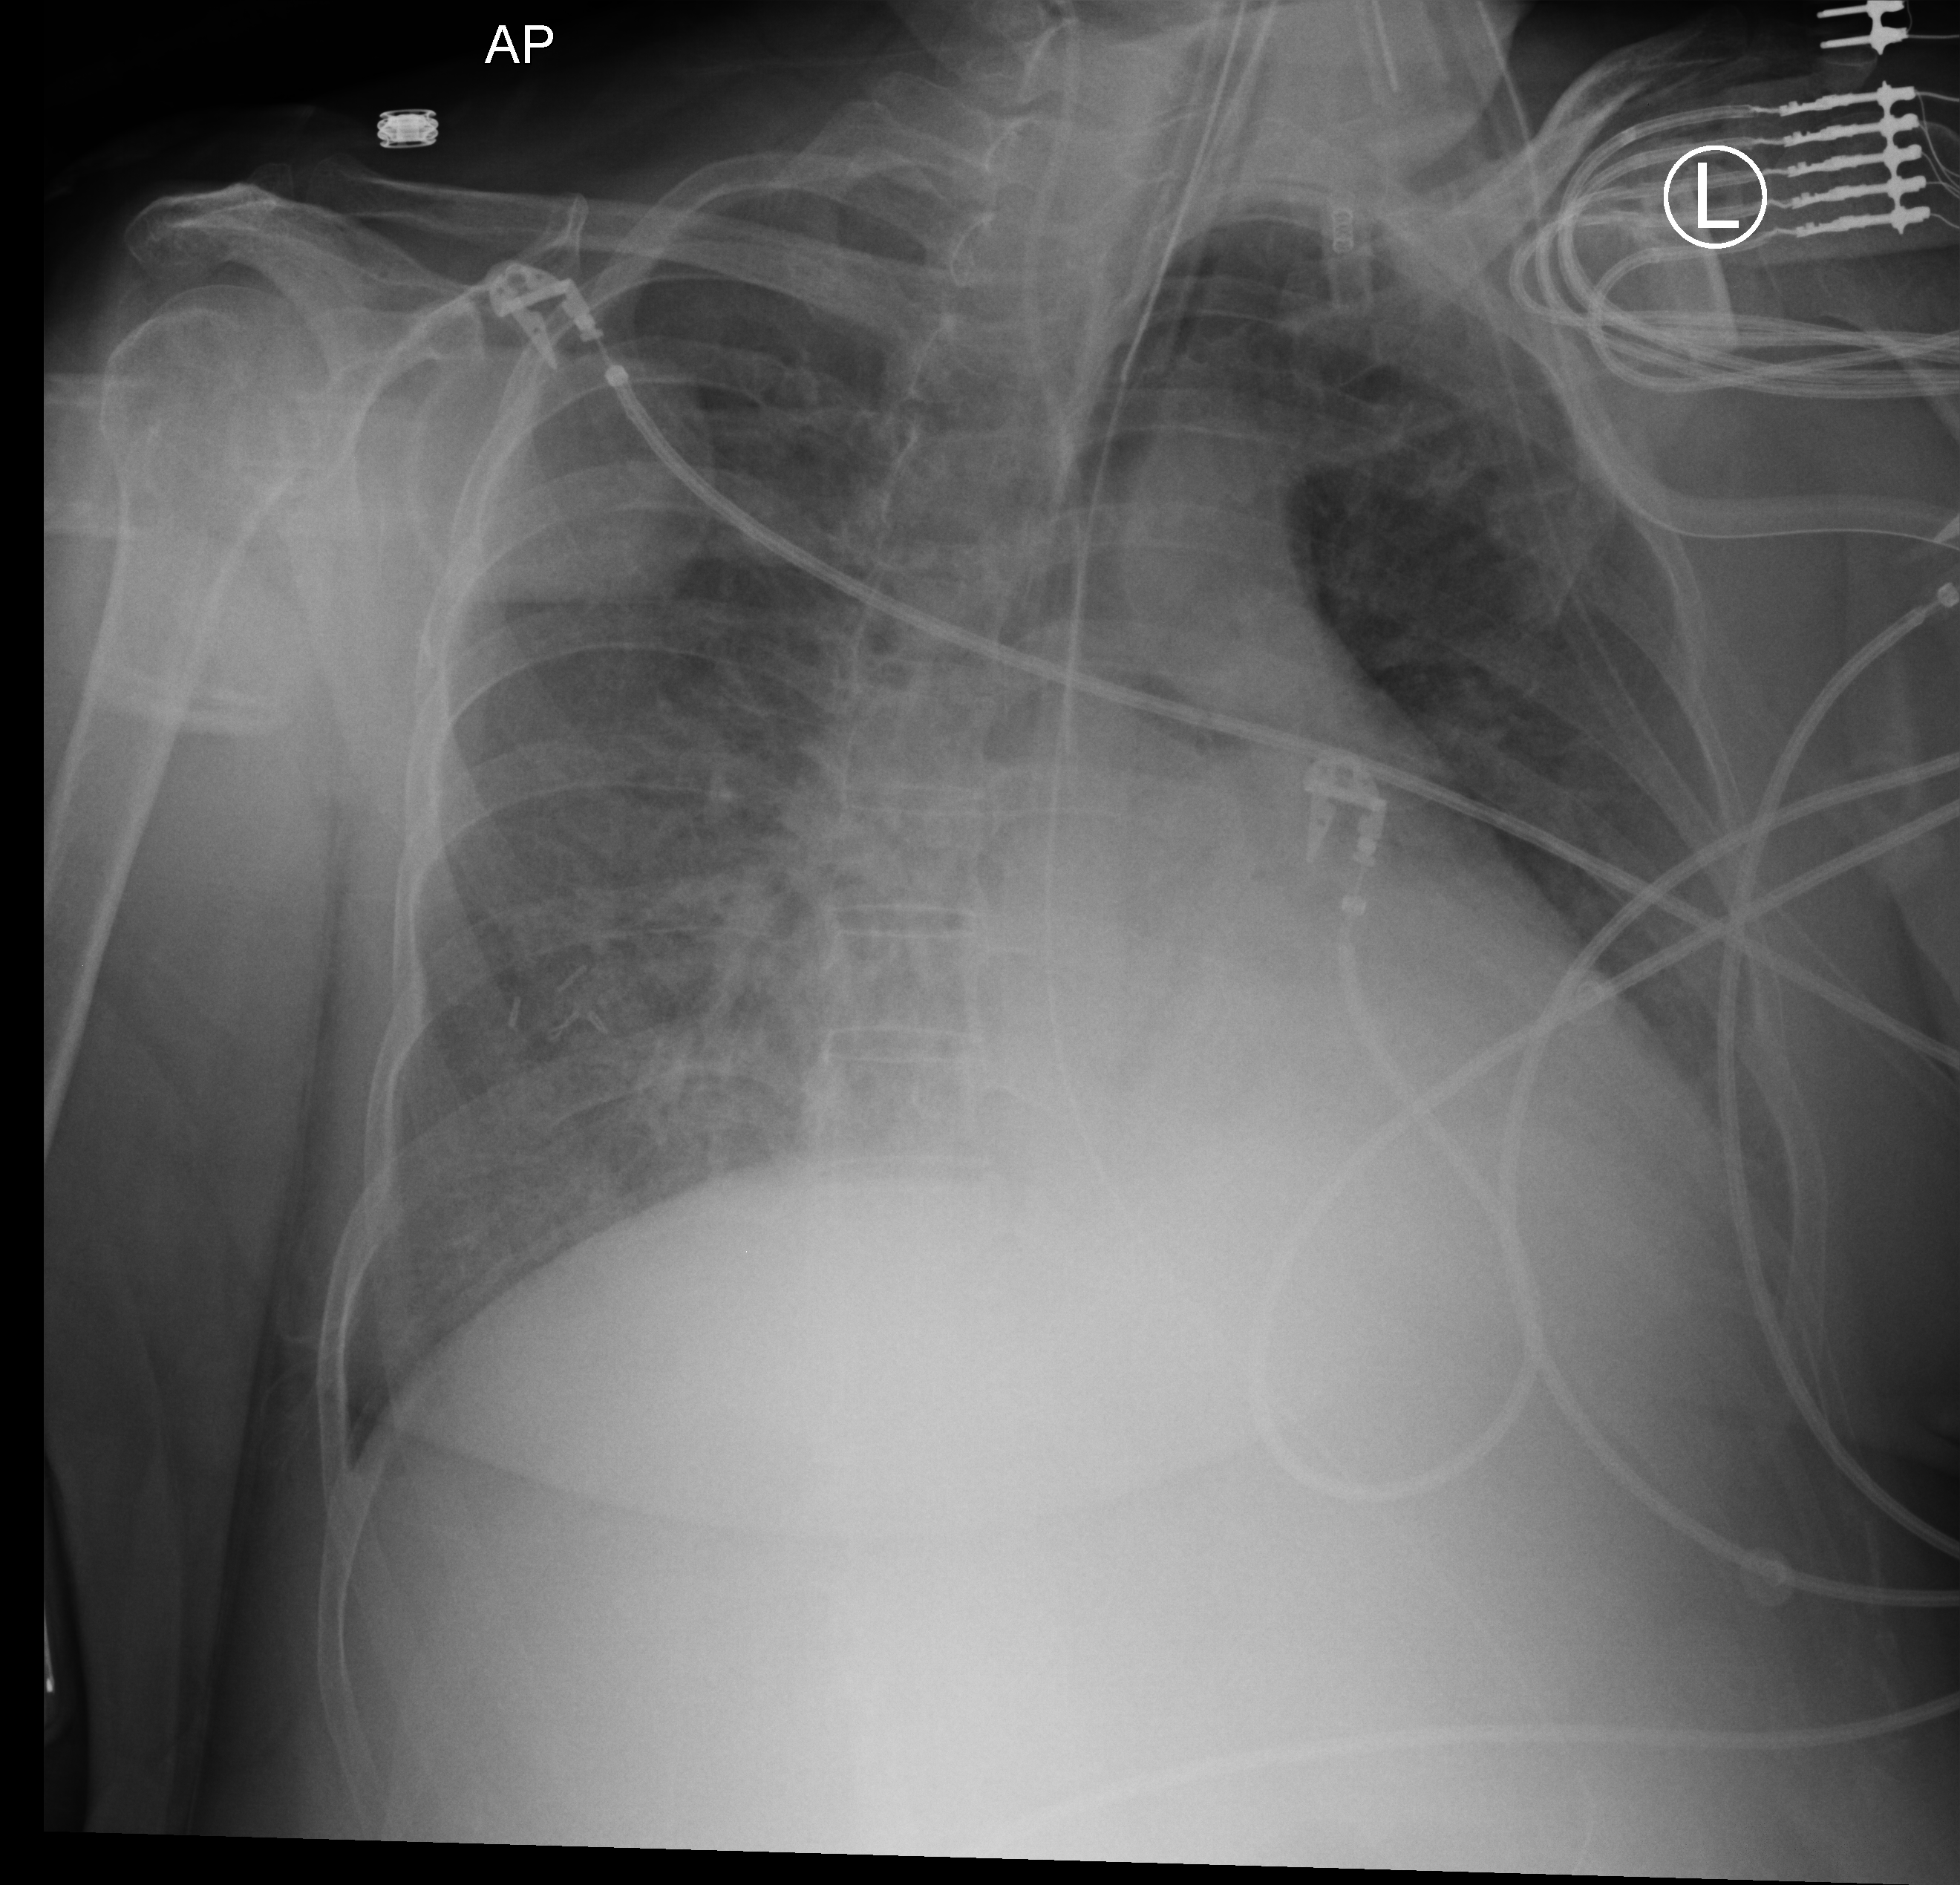
Chest X-ray (portable); anteroposterior (AP) projection. Patient hospitalised with COVID-19; female, aged 18–59 years.
Admission-level facts for this patient (not findings on this image; timing relative to this image not recorded):
- hypertension (admission record): no